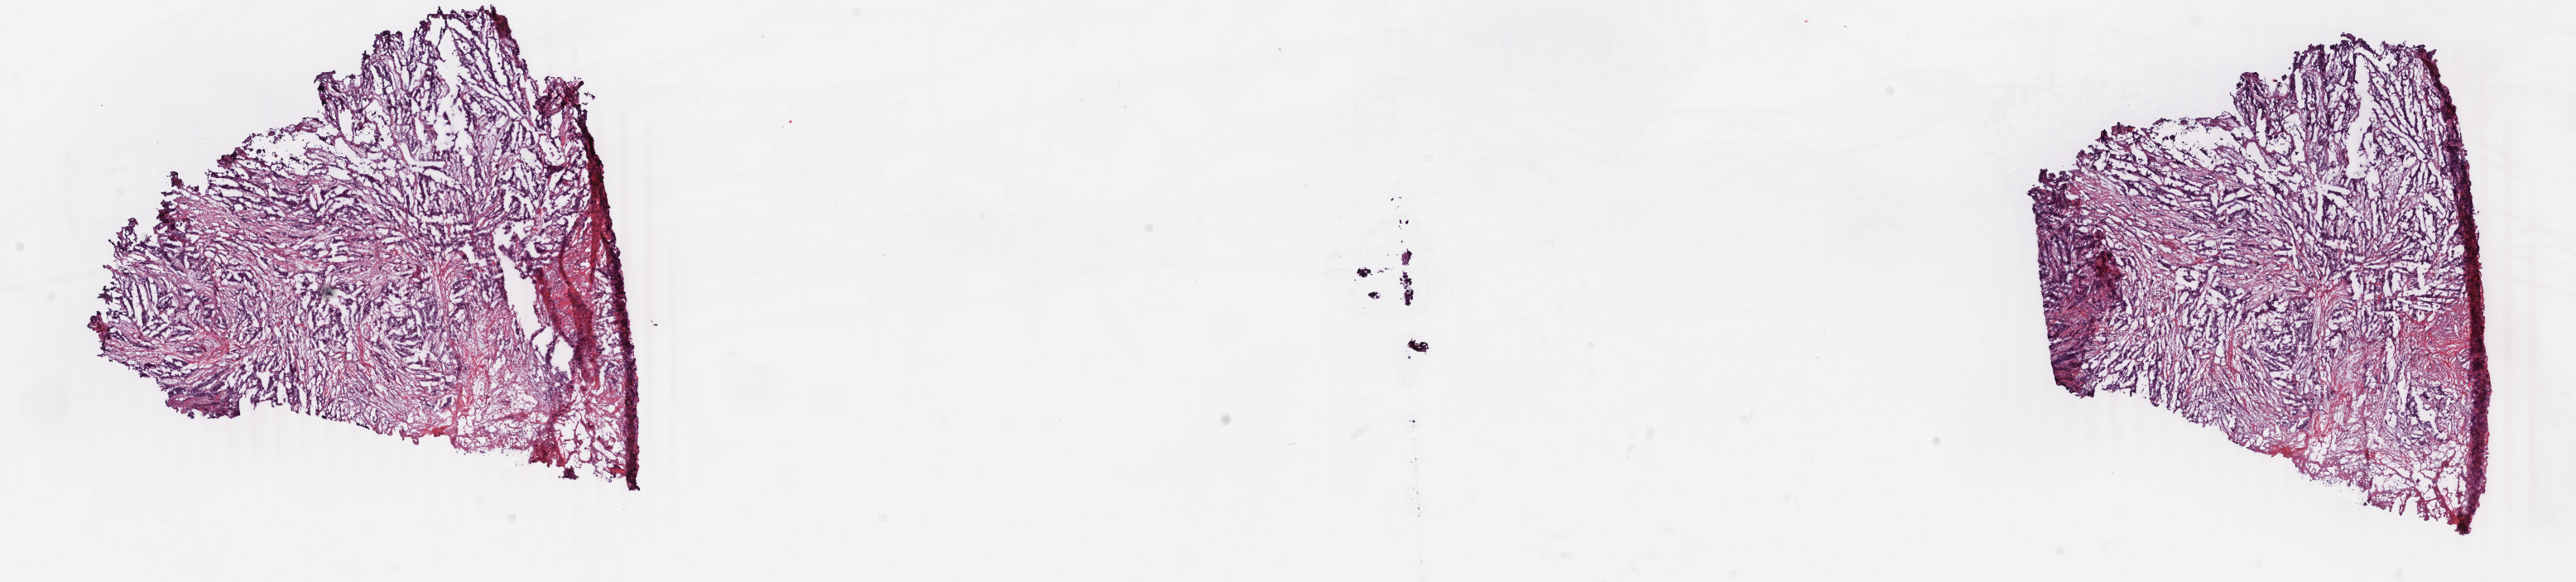
H&E-stained whole-slide image, whole scanned area (about 24.7 x 5.6 mm, acquisition: 40x scan) shown as a low-resolution overview, frozen section from the bottom of the tissue portion, breast, primary tumour sample. Female, age 47 years at initial diagnosis. Slide review estimates, as recorded: tumour cells 65%, tumour nuclei 65%, normal cells 0%, stromal cells 32%, necrosis 3%. Inflammatory infiltration, as recorded: lymphocyte infiltration 1%, monocyte infiltration 0%, neutrophil infiltration 0%.
Lymph nodes positive (case pathology): 0 of 3 examined. TNM: T2 N0 (i+) M0. AJCC pathologic stage: IIA (6th edition). Laterality: right. Diagnosis: Infiltrating duct carcinoma, NOS.